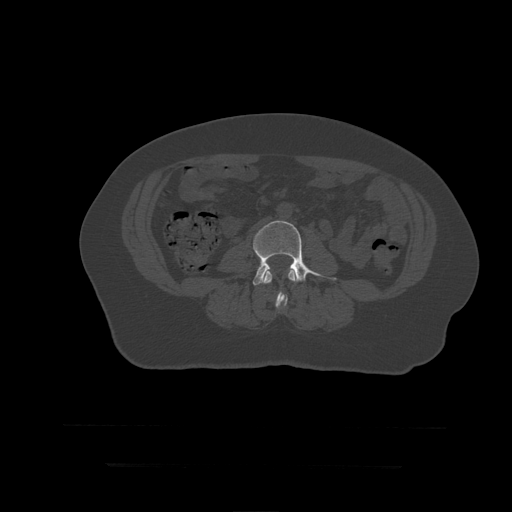
CT including the spine, one axial slice. Slice 106 of 399 in the series (ordered by position). Bone window (W 1800 / L 400 HU). 512 × 512 image matrix, field of view 450 × 450 mm. Patient age 41 years. From the clinical record (not read from this slice): primary cancer: breast.
Outlined on this slice (semi-automatically segmented with operator editing):
- L3 vertebra: bounding box (x1, y1, x2, y2) in pixels: (262, 269, 297, 309)
- L4 vertebra: (253, 221, 337, 295)